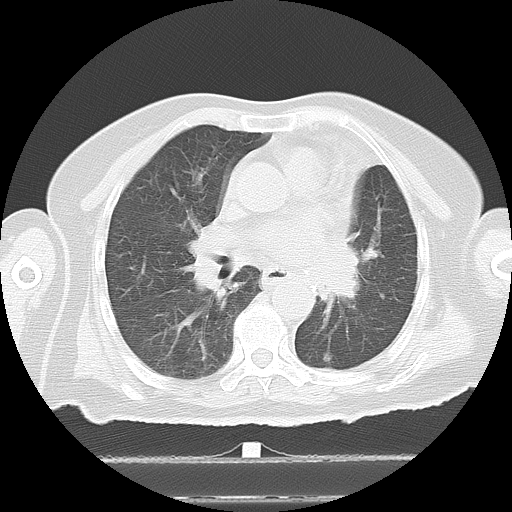
Chest CT, one axial slice; slice 7 of 27 in the series (ordered by position); reconstruction kernel LUNG; 120 kVp; lung window (W 1500 / L -600 HU); 5 mm slice thickness; 512 × 512 image matrix, field of view 350 × 350 mm. Female patient, age 67 years. Case-level facts recorded for this patient, not image findings: clinical TNM (as recorded): T1a N1 M1c.
Structures marked on this image (bounding box drawn by a radiologist):
- lung tumour (recorded histology: adenocarcinoma): bounding box [x1, y1, x2, y2] px = [325, 239, 362, 313]